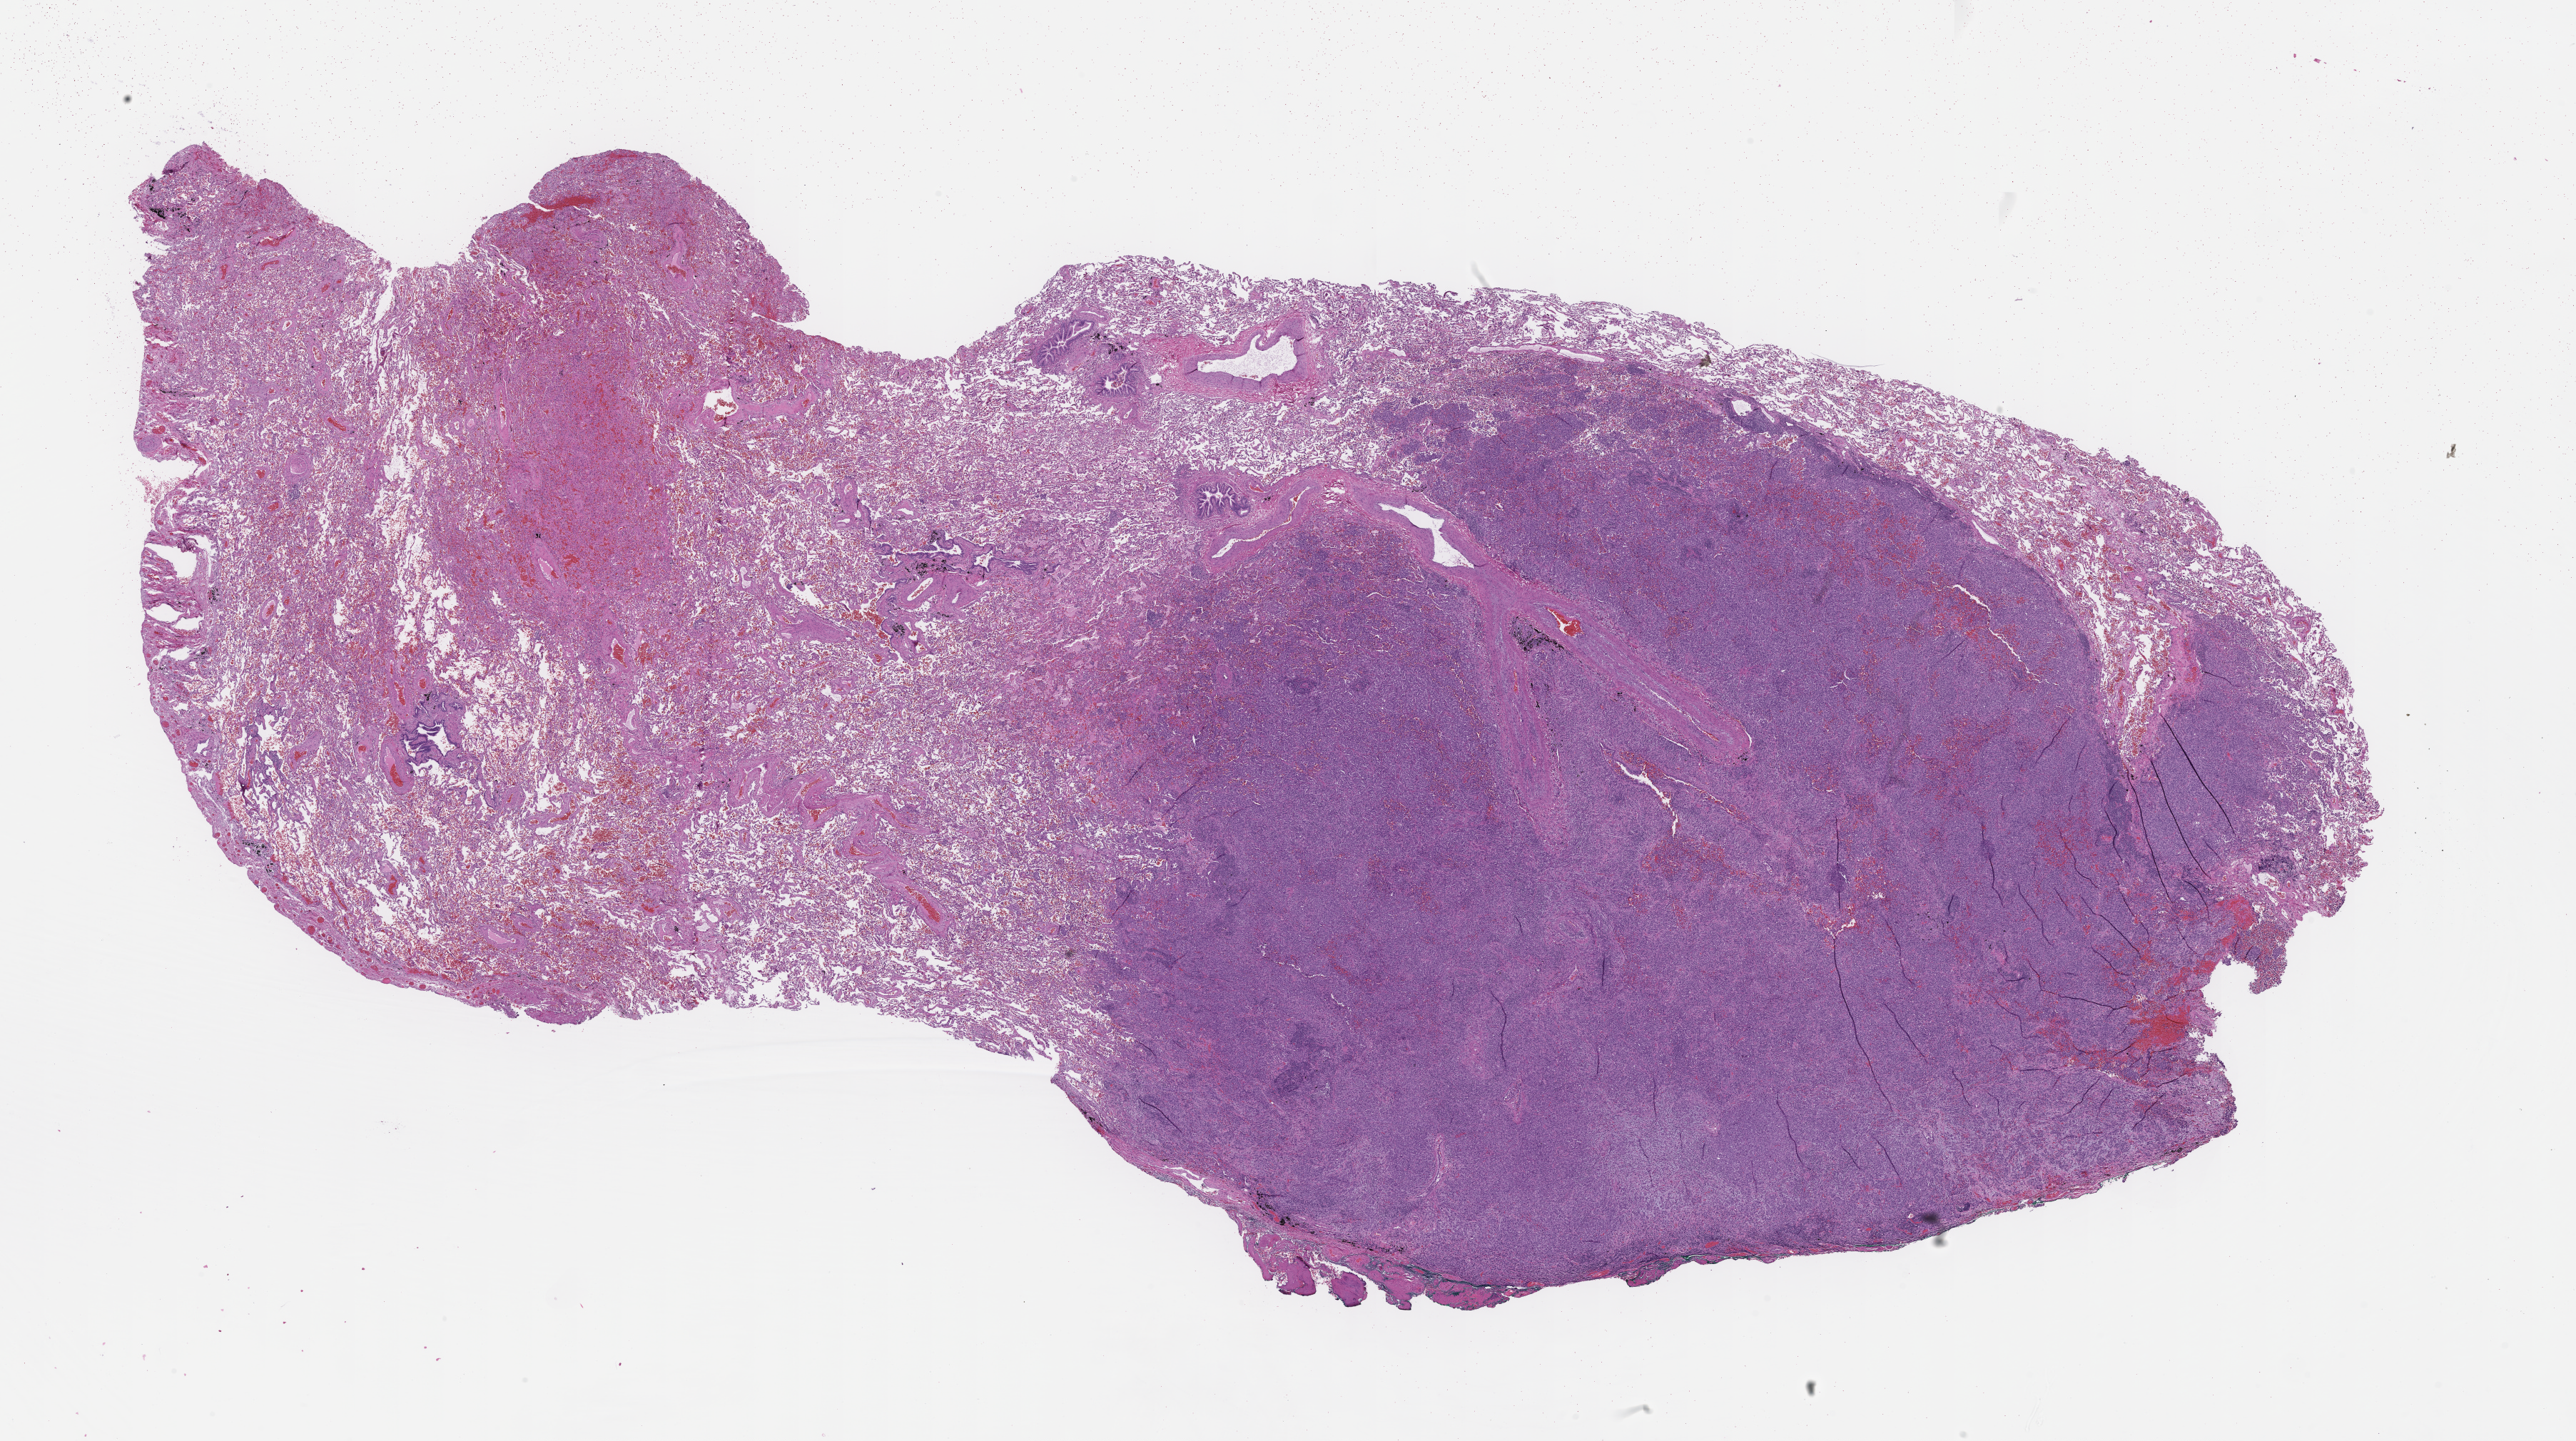
Hematoxylin and eosin (H&E) whole-slide image — shown as a low-resolution overview of the whole scanned area (about 29.1 x 16.3 mm); formalin-fixed, paraffin-embedded (FFPE) tissue; archival tissue. Patient: male.
This section: metastasis (sampled organ not recorded). Primary diagnosis of the patient: Melanoma.